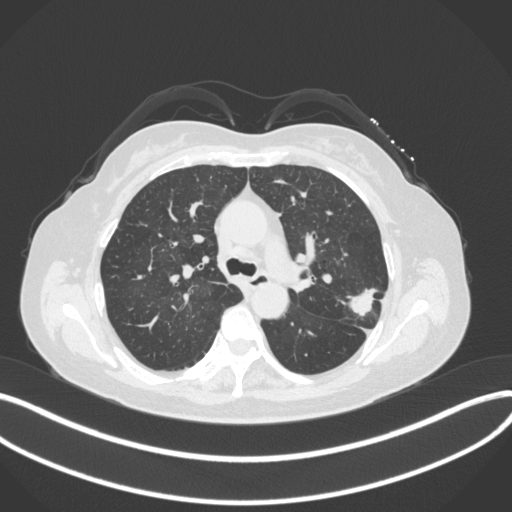
Chest CT, one axial slice; position 225 of 330 along the scan axis; reconstruction kernel B31f; 120 kVp; lung window (W 1500 / L -600 HU); 1 mm slice thickness; 512 × 512 image matrix, field of view 400 × 400 mm. Patient: female, 60 years. From the clinical record (not read from this slice): clinical TNM (as recorded): T1c N0 M0.
Structures marked on this image (rectangle marked by the reading radiologist):
- lung tumour (recorded histology: adenocarcinoma): bounding box [x1, y1, x2, y2] px = [340, 279, 376, 321]